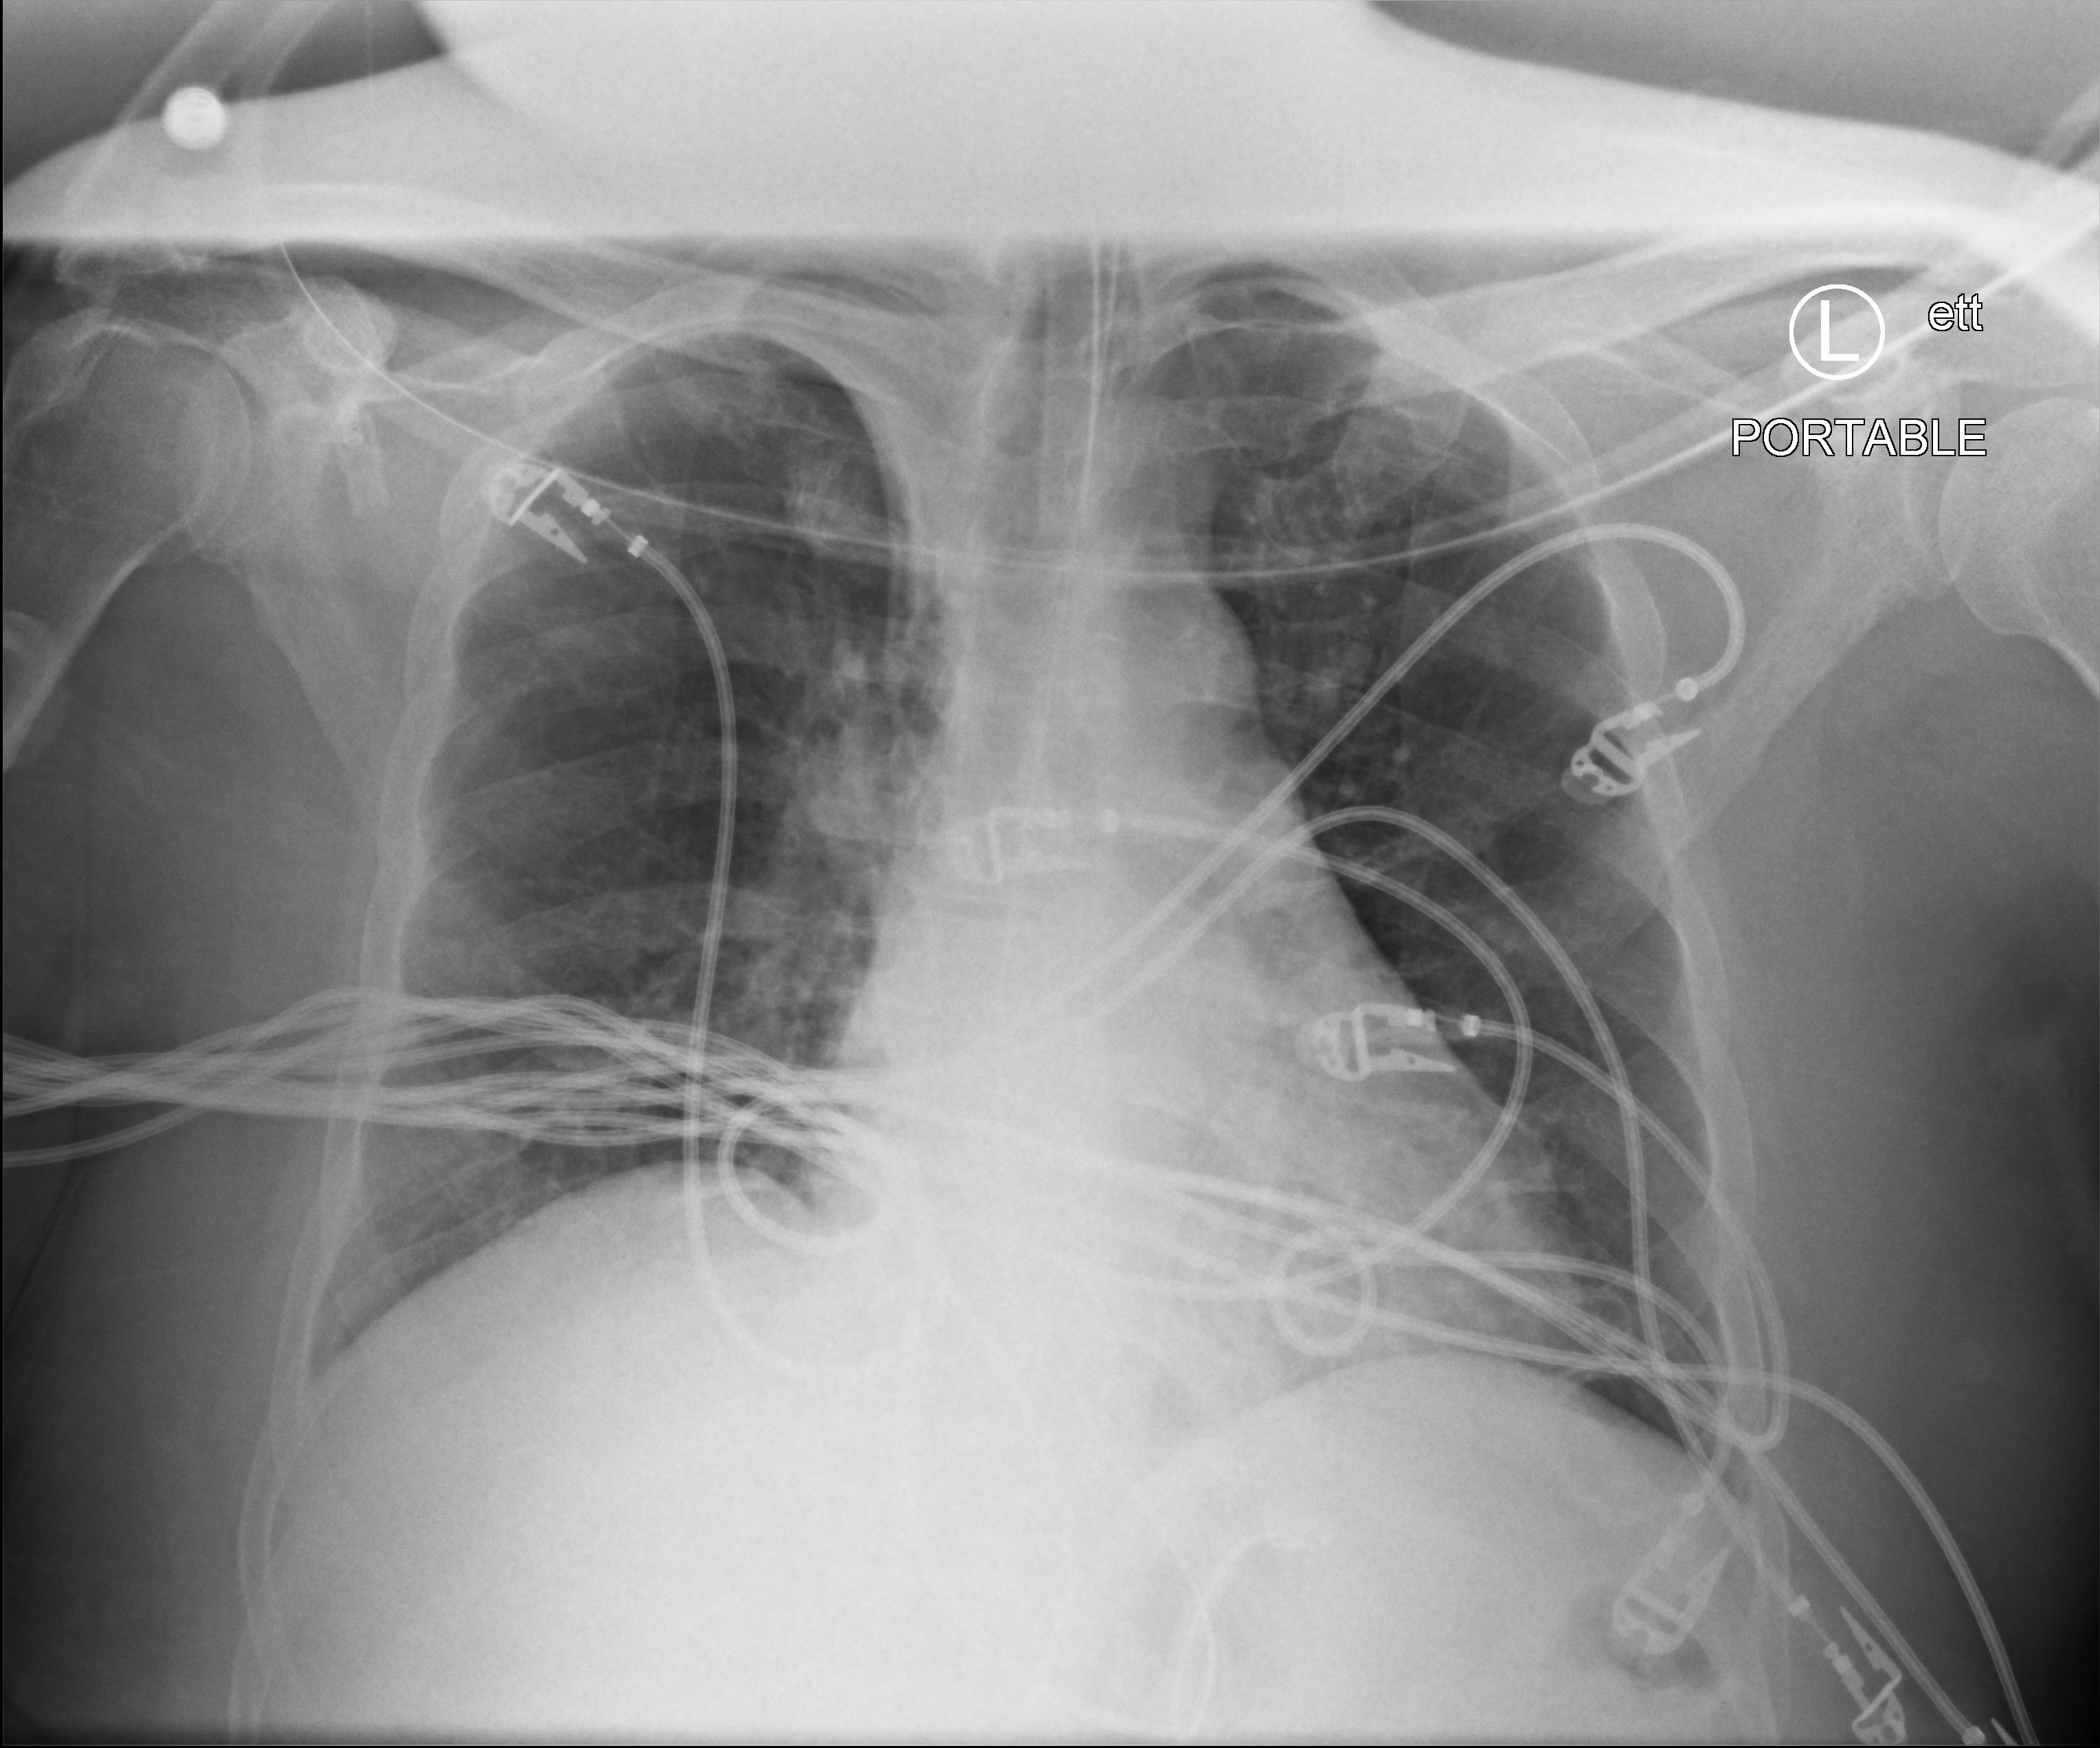
Portable chest radiograph. Adult patient hospitalised with COVID-19, age 18–59 years.
Hospital-stay facts (about this admission, not read from this image; timing relative to this image not recorded): length of hospital stay: 37 days; admitted to intensive care during this hospital stay: yes.